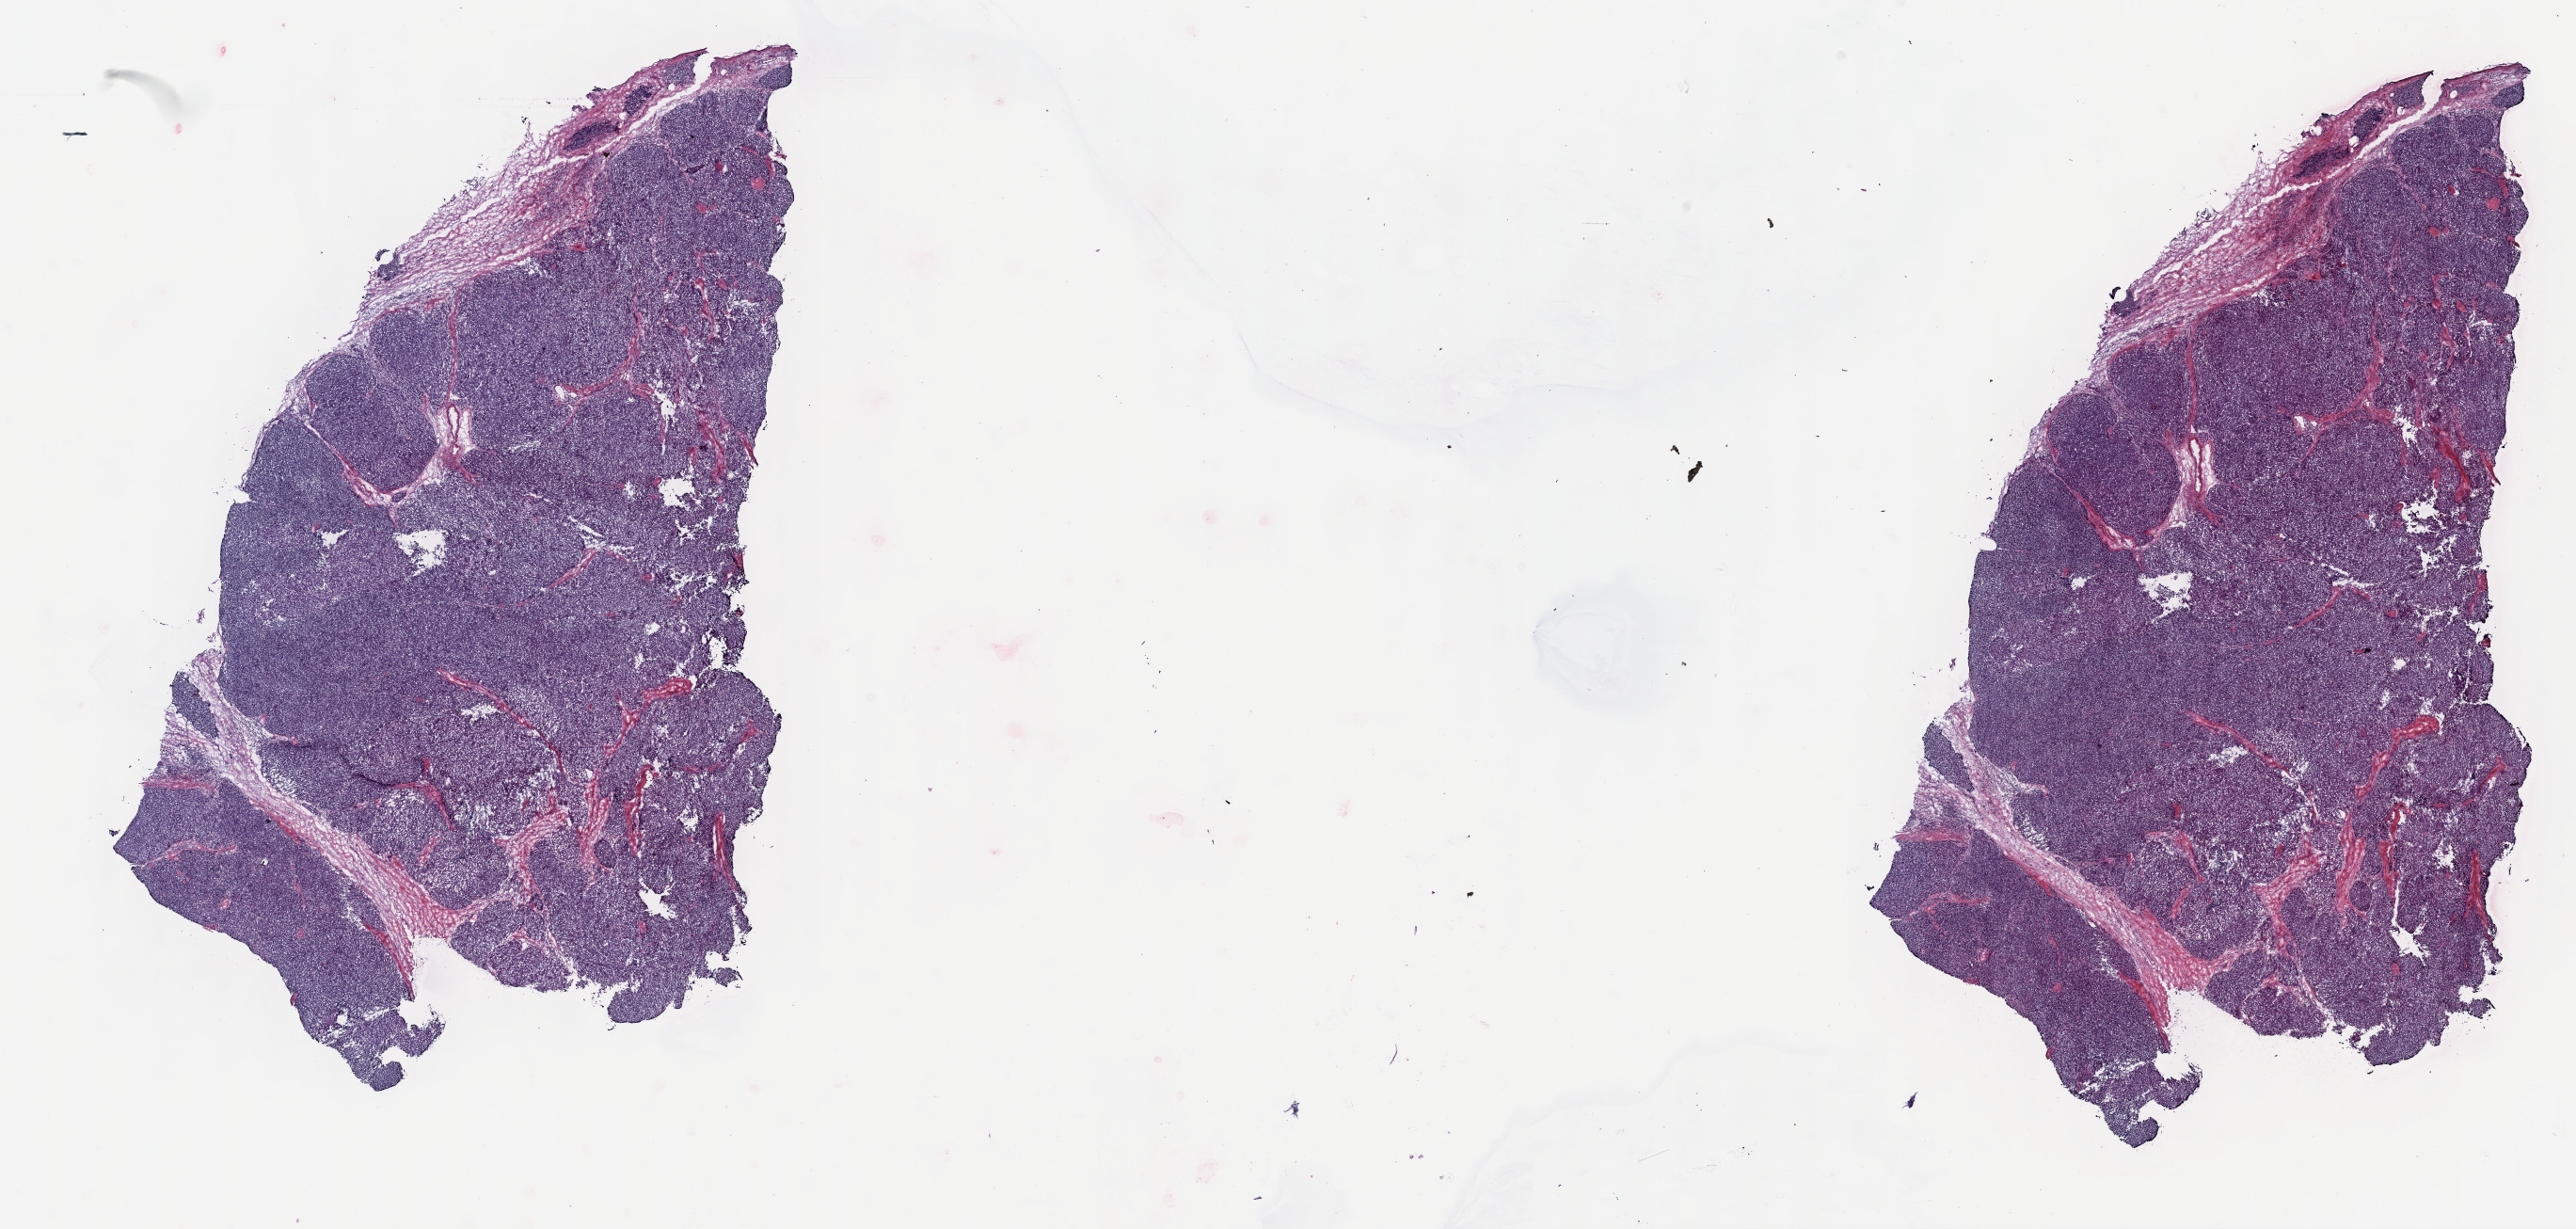
H&E-stained whole-slide image, low-resolution overview of the scanned area, about 22.1 x 10.6 mm (slide scanned at 40x). Frozen section from the top of the tissue portion. Thymus, primary tumour sample. Male, age 54 years at initial diagnosis. Pathologist review of this section (percent, as recorded): tumour cells 95%, tumour nuclei 95%, normal cells 0%, stromal cells 5%, necrosis 0%. Inflammatory infiltration, as recorded: lymphocyte infiltration 0%, monocyte infiltration 0%, neutrophil infiltration 0%.
Histologic diagnosis: Thymoma, type A, malignant.